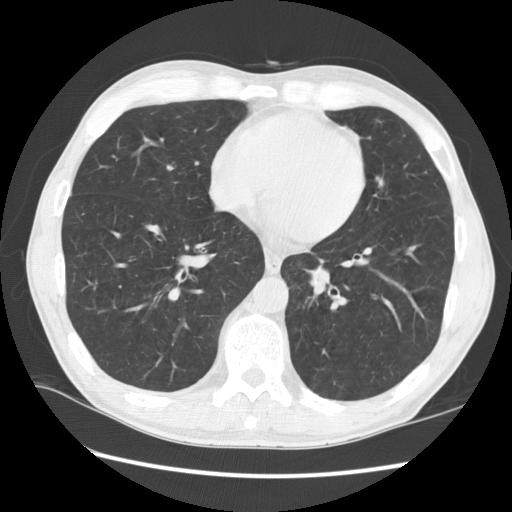
Low-dose screening chest CT, axial slice; first (baseline) screen; lung window (W 1500 / L -600 HU); 2.5 mm slice thickness; 120 kVp; slice 94 of 141 in the series. Male participant, aged 57 years at enrolment. Current smoker at enrolment.
Lesion marked by an expert reader, box from (x=268, y=248) to (x=344, y=313) px. The screening reader recorded 2 non-calcified nodules or masses ≥4 mm on this exam; which of them this box marks is not recorded.